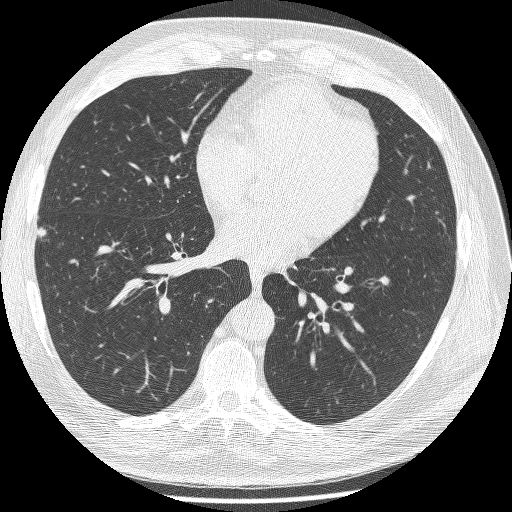
Low-dose screening chest CT, one axial slice; slice 107 of 241 in the series (ordered by position); 120 kVp; lung window (W 1500 / L -600 HU); 1.25 mm slice thickness; 512 × 512 image matrix.
Annotated regions visible in this slice (manually delineated by an expert):
- lesion 1 (tumor, lower lobe of right lung): box from (x=37, y=227) to (x=47, y=239) px